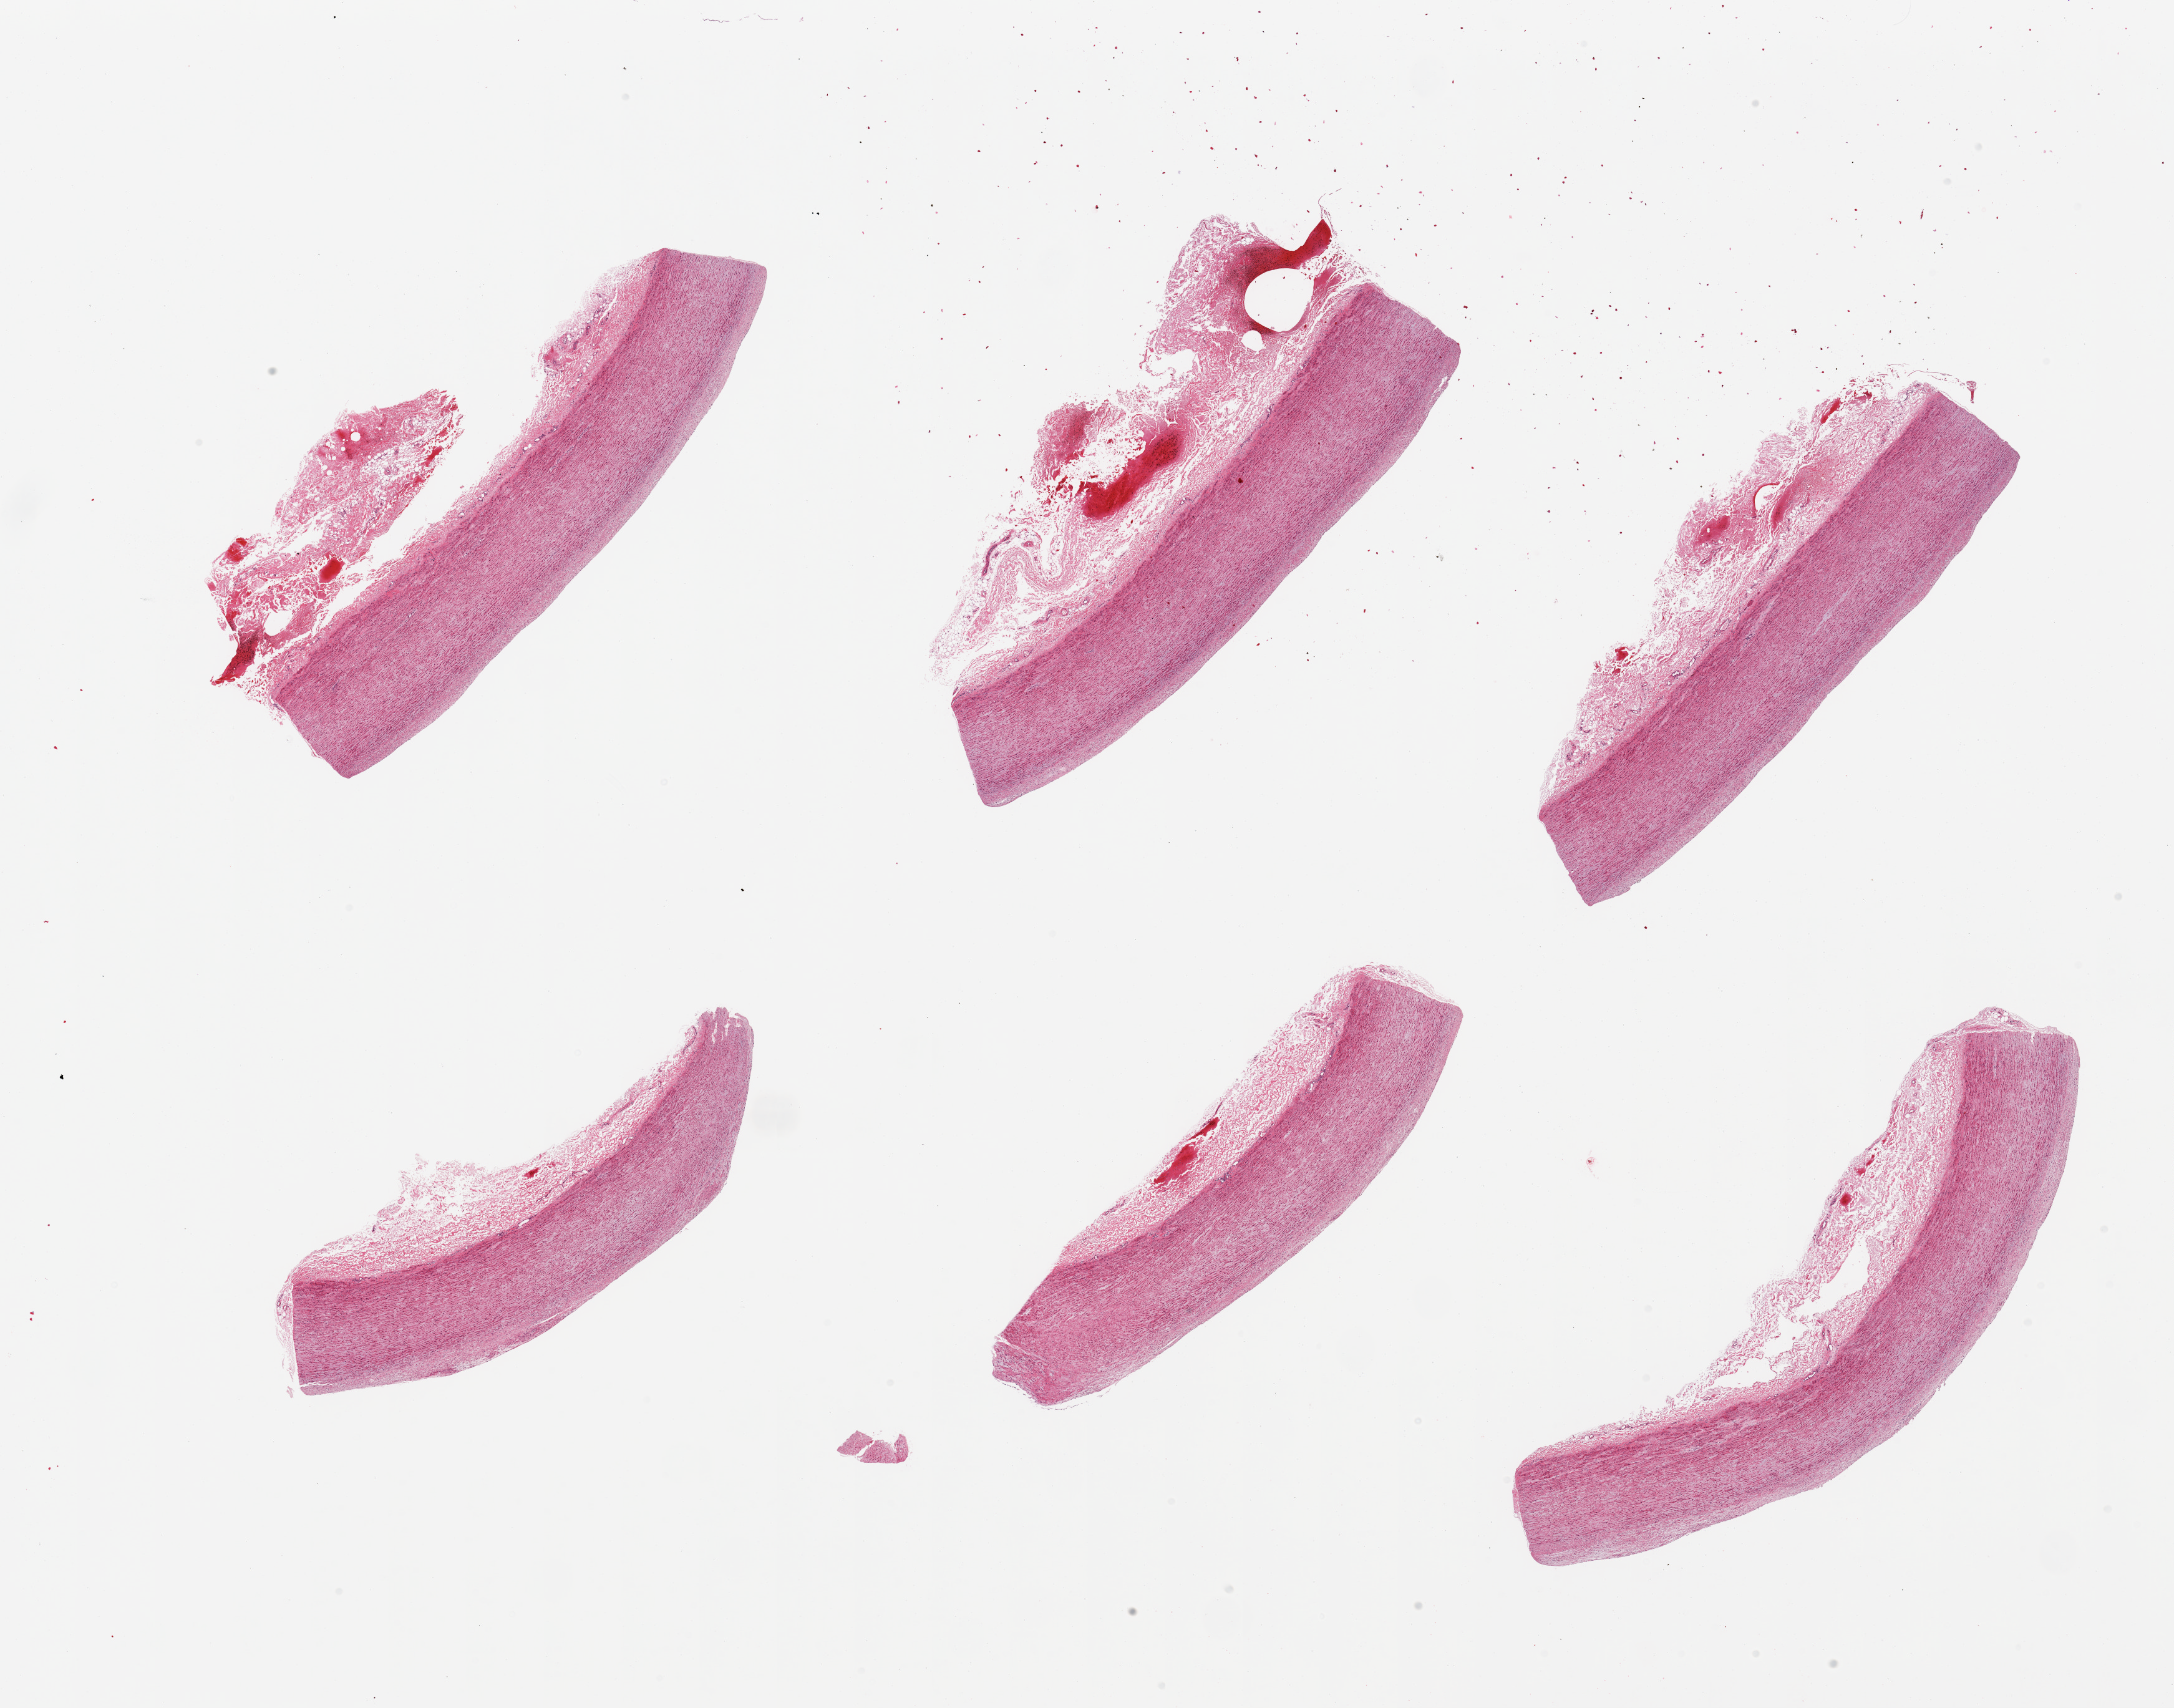
Hematoxylin and eosin (H&E) whole-slide image, brightfield — a low-resolution overview of the entire scanned area, about 27.6 x 21.7 mm, PAXgene-fixed paraffin-embedded (PFPE) section, sampled site (target tissue): aorta, donor tissue sample. Donor sex: male.
• pathologist's review note for this sample: 6 pieces; mild atherosis, attached adventitia